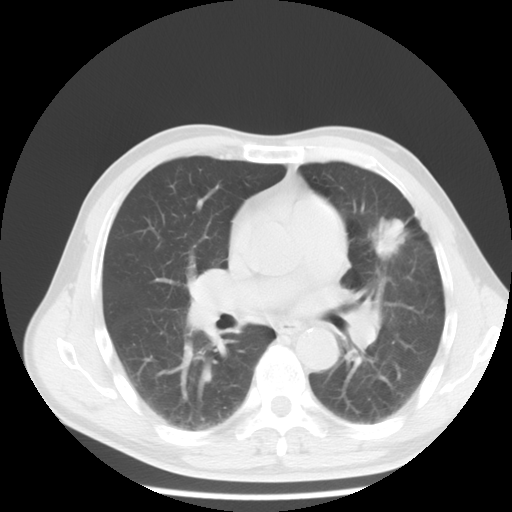
Chest CT, one axial slice; position 6 of 10 along the scan axis; lung window (W 1500 / L -600 HU); 512 × 512 image matrix. Patient: male, 54 years. From the clinical record (not read from this slice): clinical TNM (as recorded): T1c N0 M0.
Annotated regions visible in this slice (rectangle marked by the reading radiologist):
- lung tumour (recorded histology: adenocarcinoma): bounding box (x1, y1, x2, y2) in pixels: (373, 217, 408, 263)